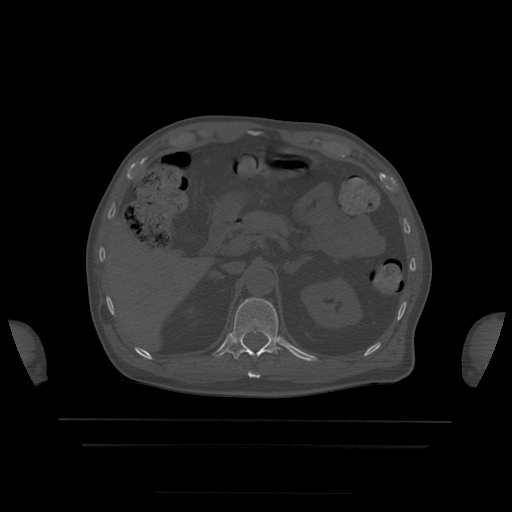
CT including the spine, one axial slice. Position 197 of 522 along the scan axis. Bone window (W 1800 / L 400 HU). 1.25 mm slice thickness. 512 × 512 image matrix. Patient age 68 years. Case-level facts recorded for this patient, not image findings: primary cancer: urothelial.
Annotated regions visible in this slice (semi-automatically segmented with operator editing):
- T11 vertebra: box from (x=248, y=372) to (x=261, y=379) px
- T12 vertebra: (x=228, y=298)–(x=283, y=360)